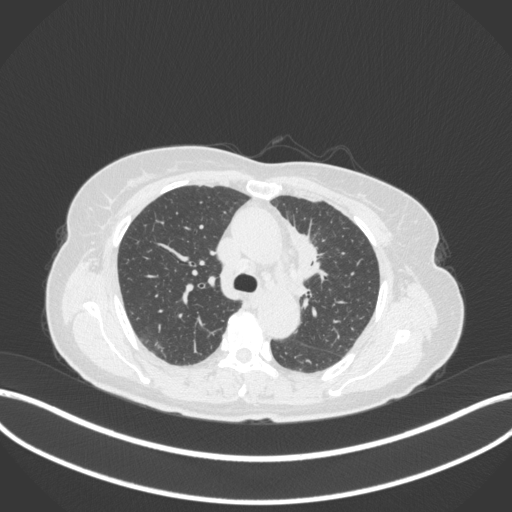
Chest CT, one axial slice. Slice 228 of 368 in the series (ordered by position). Reconstruction kernel B31f. Lung window (W 1500 / L -600 HU). 1 mm slice thickness. 512 × 512 image matrix, field of view 400 × 400 mm. Female patient, age 65 years. From the clinical record (not read from this slice): clinical TNM (as recorded): T2a N0 M0; histopathological grade: G2-3.
Outlined on this slice (bounding box drawn by a radiologist):
- lung tumour (recorded histology: adenocarcinoma): bounding box [x1, y1, x2, y2] px = [292, 231, 322, 281]